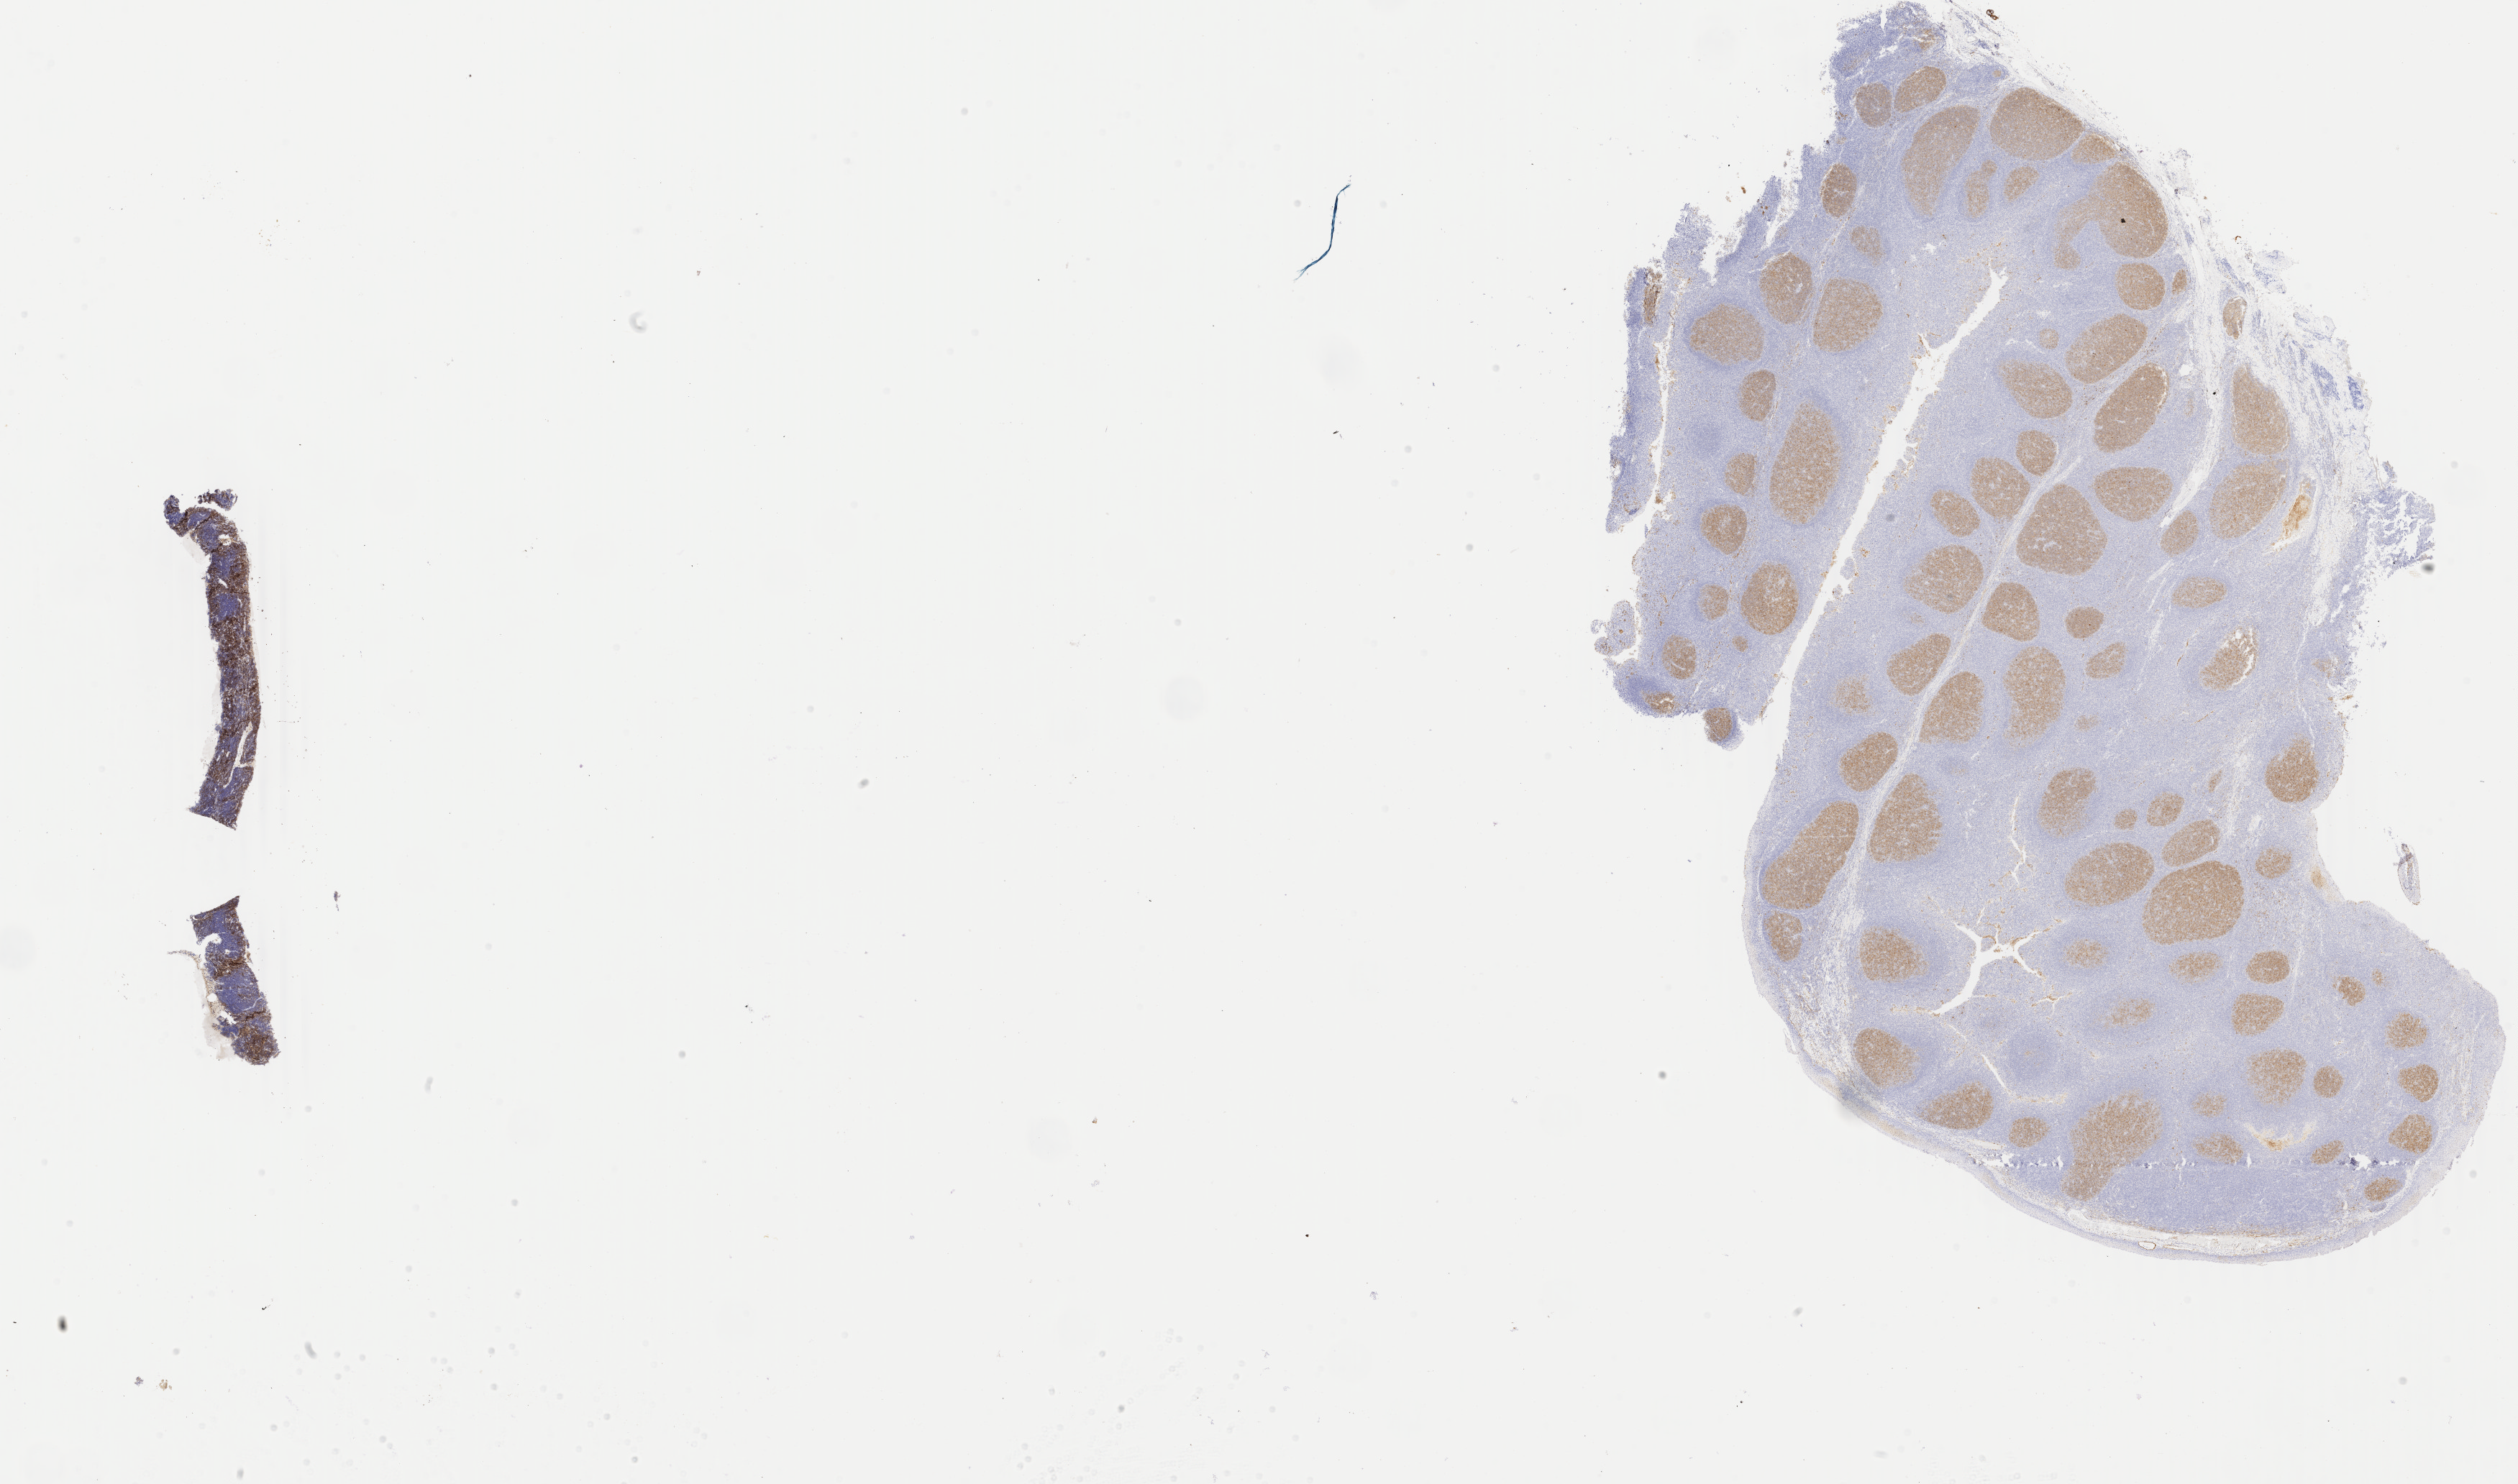
Immunohistochemistry (IHC) whole-slide image stained for CD10, shown as a low-resolution overview of the whole scanned area (about 27.8 x 16.4 mm), specimen: tumor tissue, anatomic site: abdominal lymph node. Patient: female, age at initial diagnosis 6 years.
Histologic diagnosis: Burkitt lymphoma, NOS.